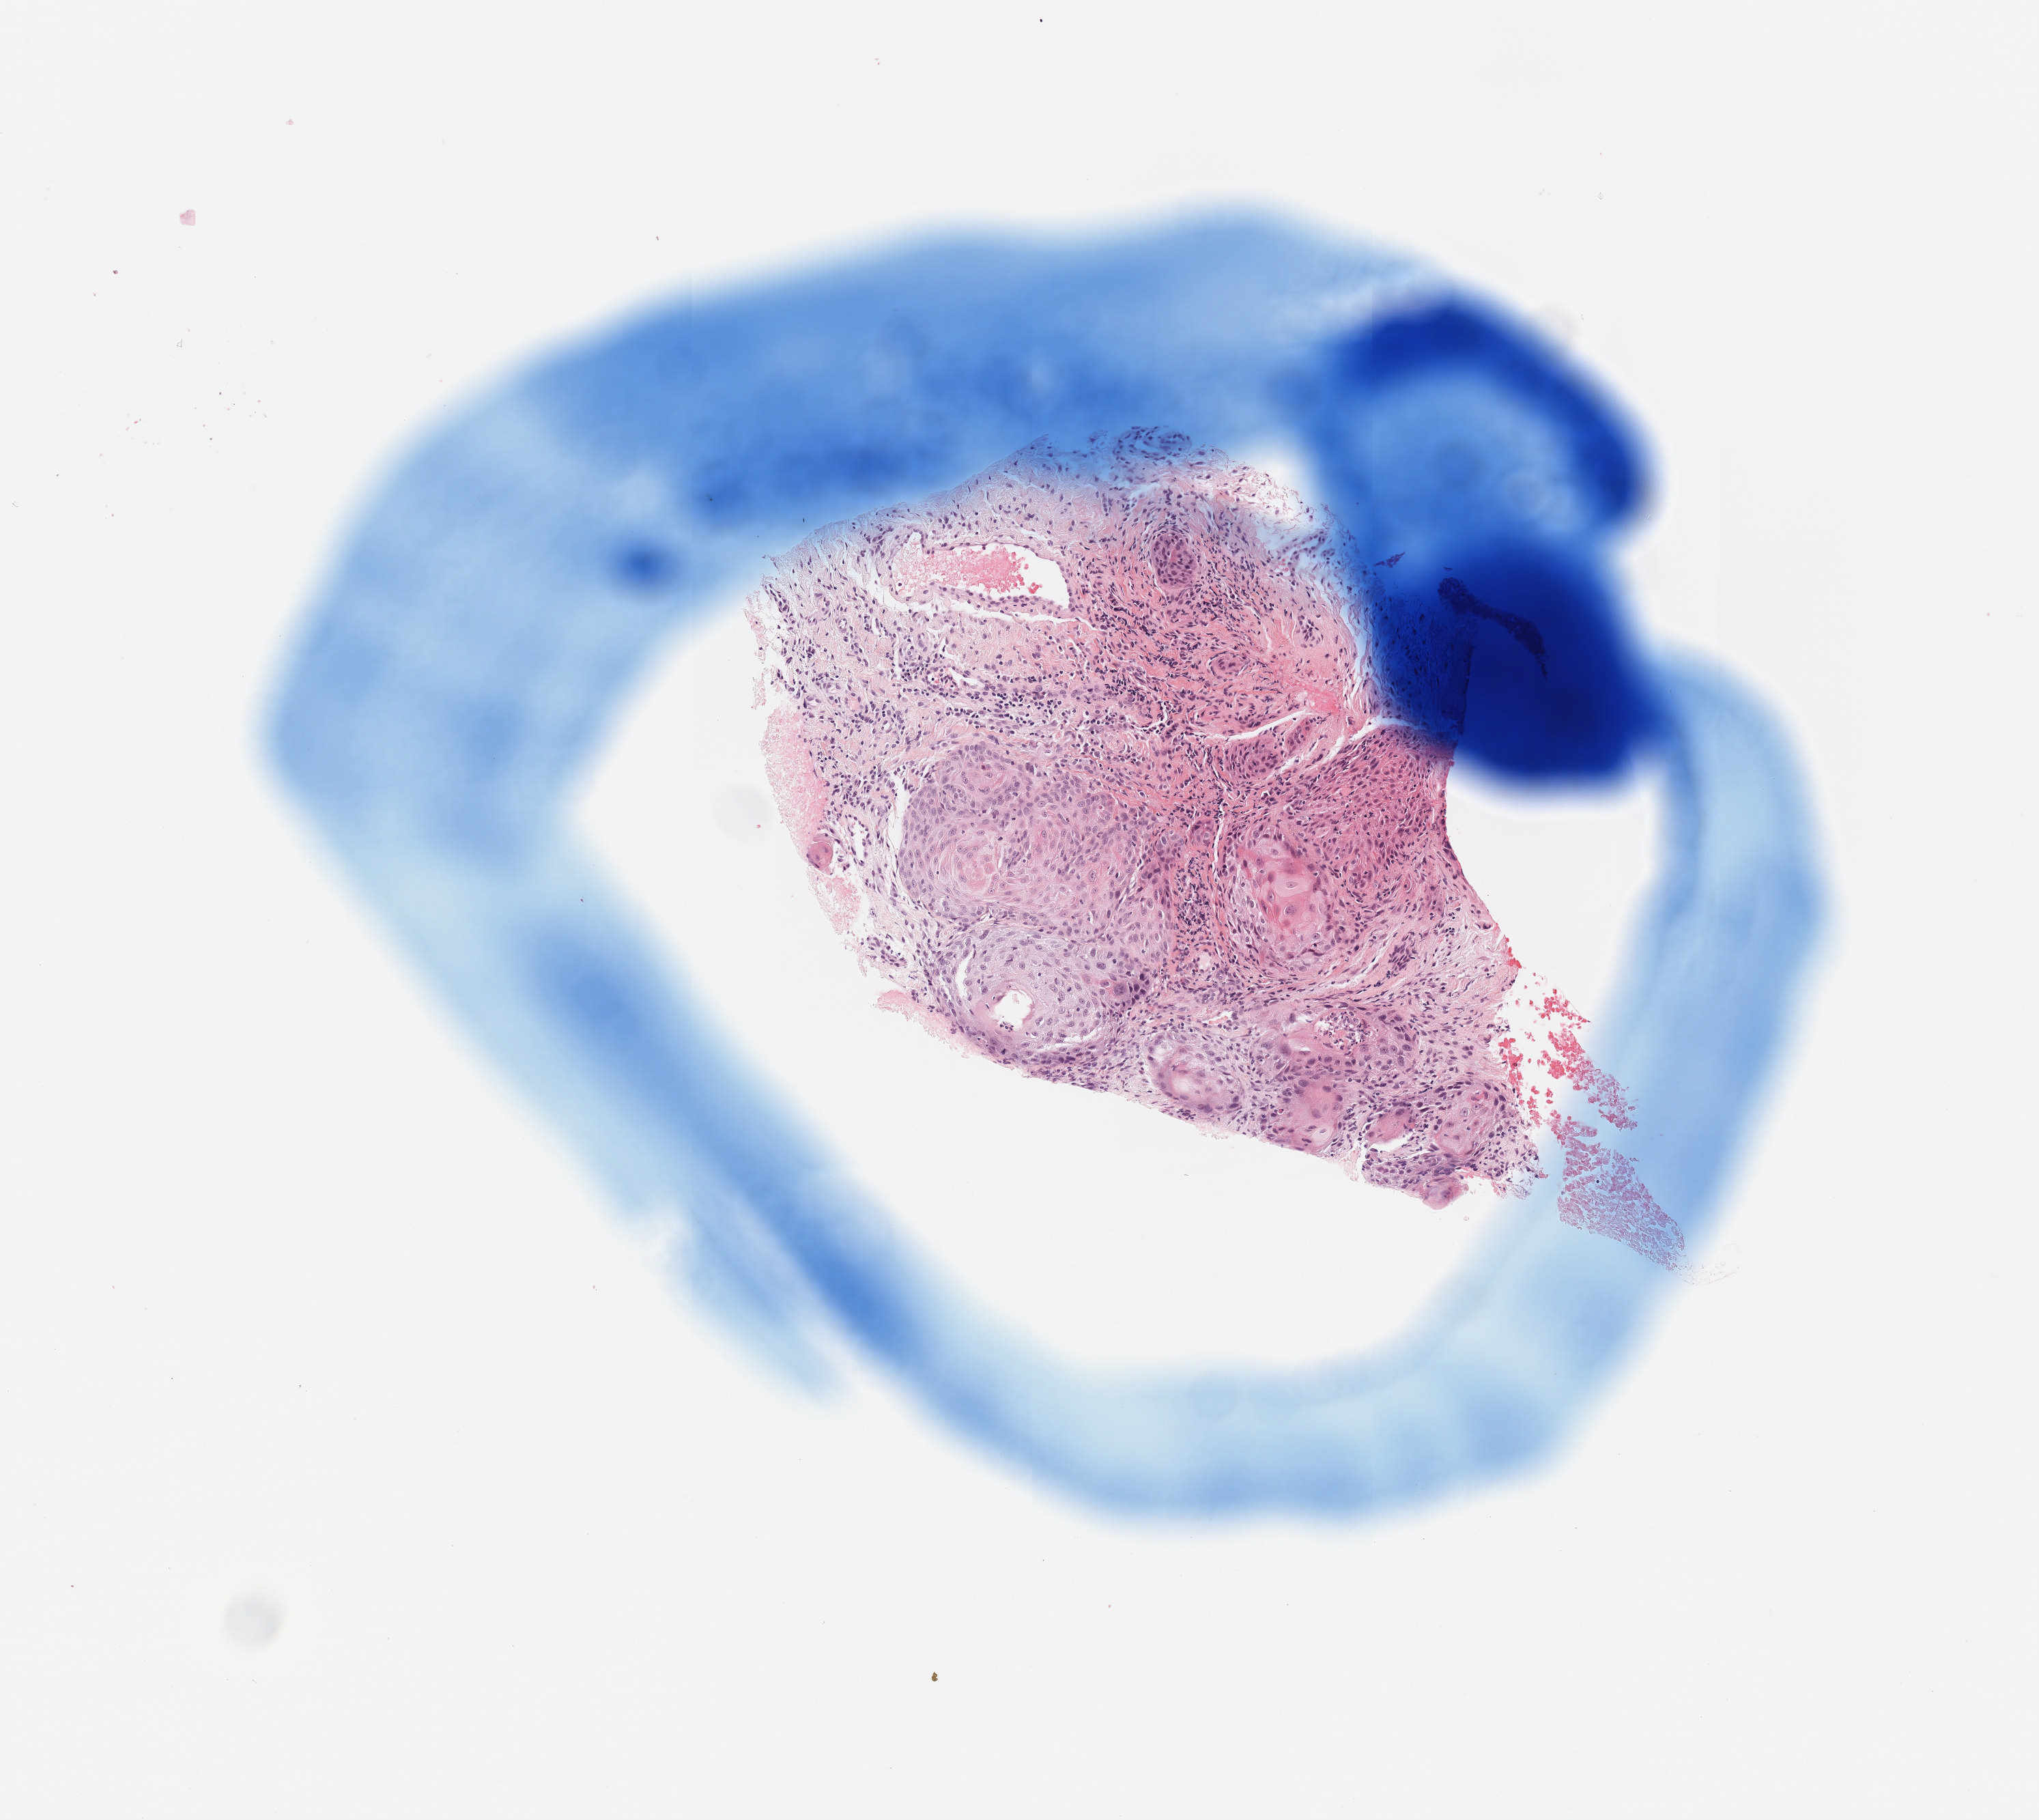
Whole-slide histology image, H&E — shown as a low-resolution overview of the whole scanned area (about 3.0 x 2.7 mm, slide scanned at 40x). Formalin-fixed paraffin-embedded (FFPE) diagnostic section. Primary tumour sample from the head and neck. Male patient; age at initial diagnosis 73 years. Histologic grade: G2 (moderately differentiated).
• pathologic diagnosis: Squamous cell carcinoma, NOS (tongue, NOS)